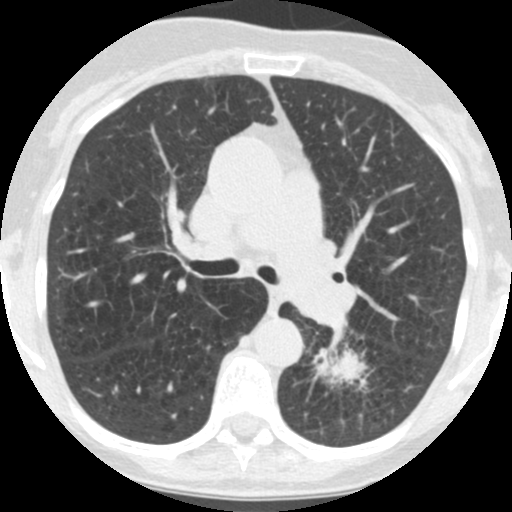
Chest CT (low-dose screening protocol), one axial image. Third annual screen. Lung window (W 1500 / L -600 HU). 2.5 mm slice thickness. Standard (soft-tissue) reconstruction kernel (STANDARD). Slice 62 of 171 in the series. 512 × 512 image matrix, field of view 280 × 280 mm. Female, age 71 years at enrolment.
Lesion marked by an expert reader, bounding box <306,324,385,409> (left, top, right, bottom; pixels). The screening reader recorded 2 non-calcified nodules or masses ≥4 mm on this exam (left lower lobe, left lower lobe); which of them this box marks is not recorded. Official screen result: positive, other. Participant outcome: lung cancer diagnosed 26 days after this screen — squamous cell carcinoma, NOS, left lower lobe, poorly differentiated (G3), stage IB (AJCC 6th edition), 40 mm at pathology.